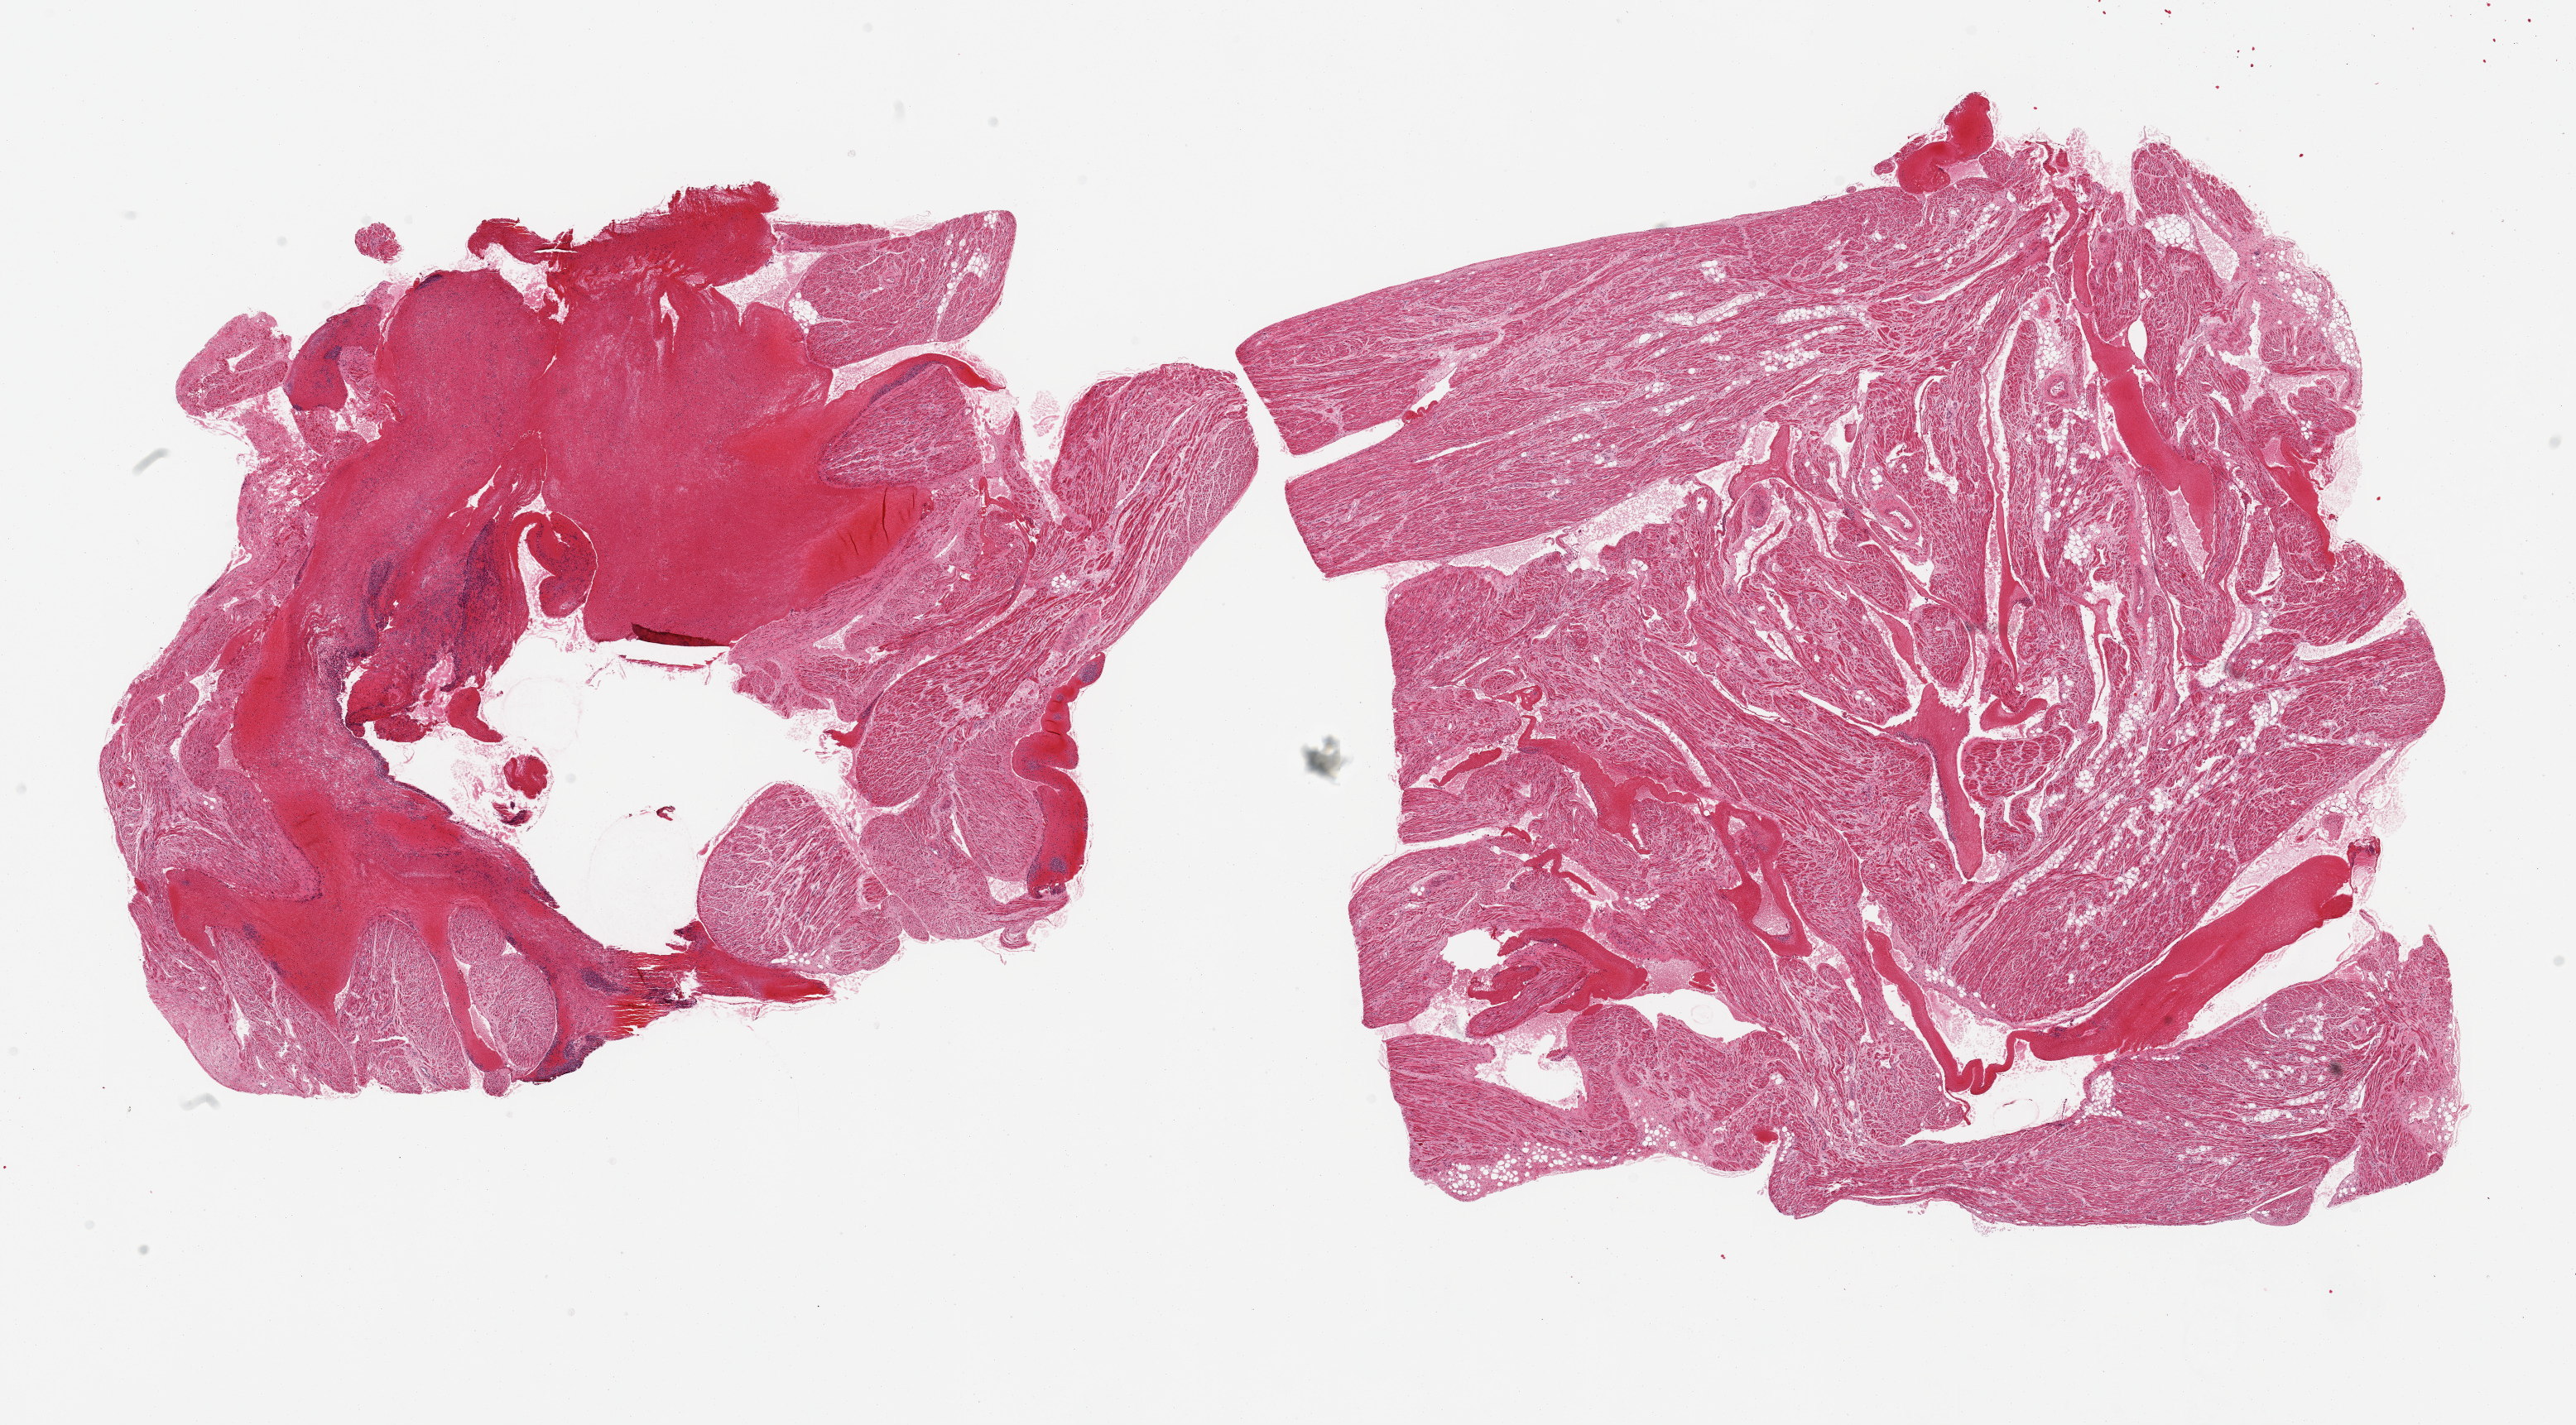
Digitized H&E-stained section, brightfield, a low-resolution overview of the entire scanned area, about 24.6 x 13.6 mm (from a 20x scan), PAXgene-fixed paraffin-embedded (PFPE) section, sampled site (target tissue): auricular appendage, tissue donor sample.
Pathologist's review note for this sample: 2 pieces; one is largely blood/clot.